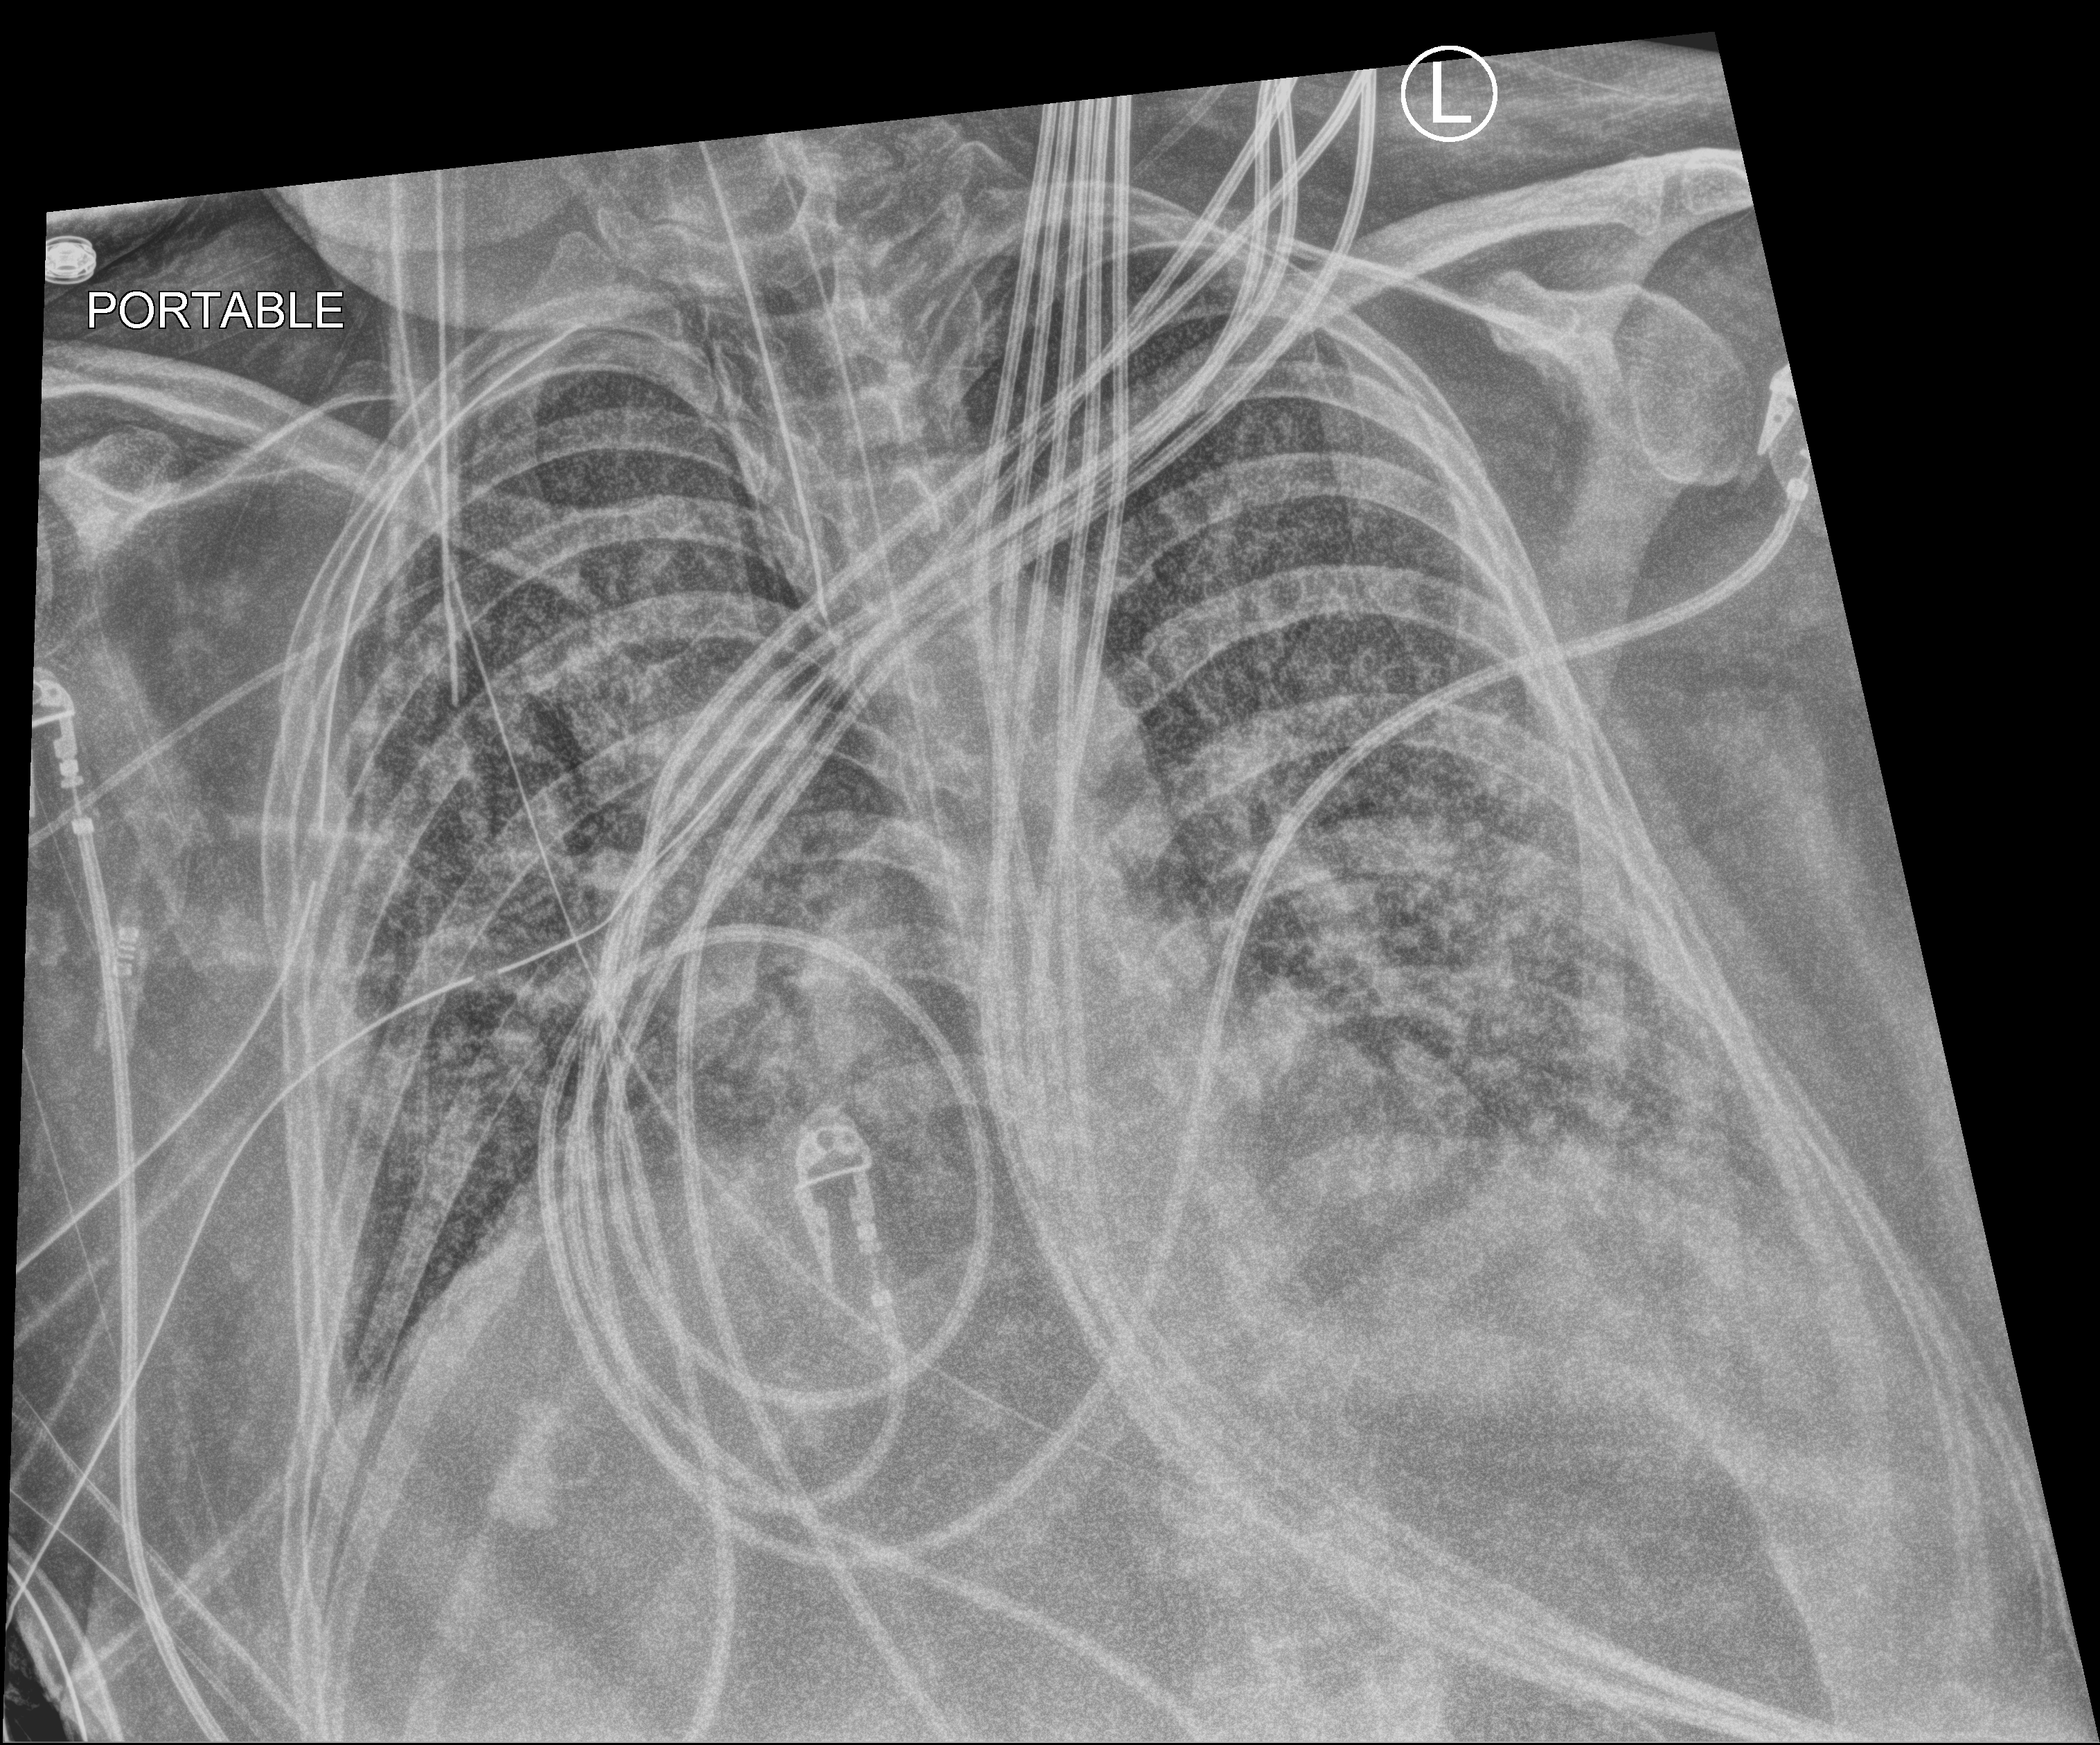
Portable chest radiograph. Adult patient hospitalised with COVID-19, age 18–59 years.
Hospital-stay facts (about this admission, not read from this image; timing relative to this image not recorded): other chronic lung disease (admission record): no.